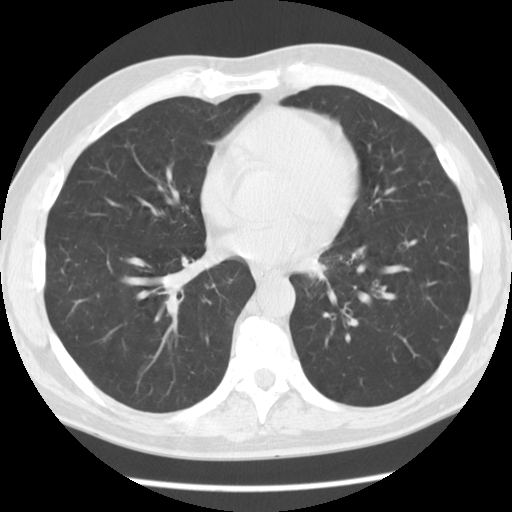
Low-dose screening chest CT, axial slice. Baseline annual screen. Lung window (W 1500 / L -600 HU). 120 kVp. Slice 68 of 112 in the series. Male, age 55 years at enrolment. Former smoker at enrolment.
Lesion marked by an expert reader, box from (x=285, y=235) to (x=344, y=291) px. Screening reader's record for this exam: no non-calcified nodule ≥4 mm recorded. Lung cancer was diagnosed 223 days after this screen: squamous cell carcinoma, NOS, left lower lobe, moderately differentiated (G2), stage IV (AJCC 6th edition), 51 mm at pathology.